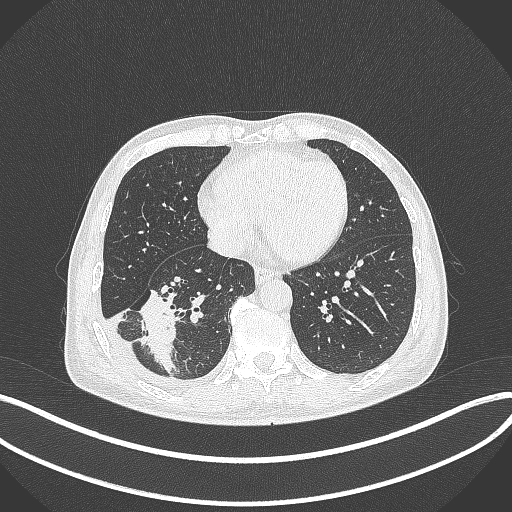
Chest CT, one axial slice. Slice 131 of 388 in the series (ordered by position). 120 kVp. Lung window (W 1500 / L -600 HU). 1 mm slice thickness. 512 × 512 image matrix, field of view 400 × 400 mm. Patient: male, 64 years. Case-level facts recorded for this patient, not image findings: clinical TNM (as recorded): T3 N0 M0; histopathological grade: G2-3.
Outlined on this slice (rectangle marked by the reading radiologist):
- lung tumour (recorded histology: adenocarcinoma): bounding box (x1, y1, x2, y2) in pixels: (140, 286, 179, 377)